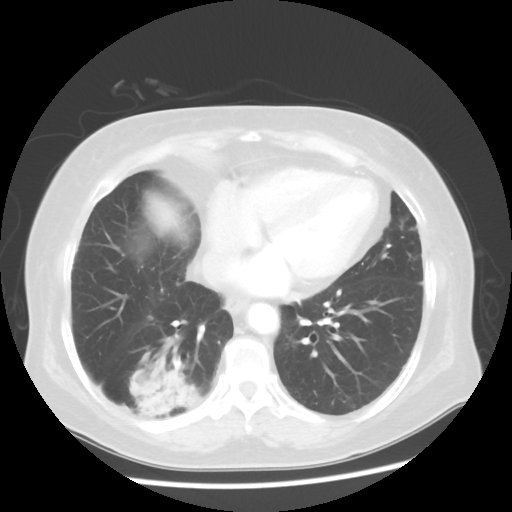
Chest CT, one axial slice. Slice 20 of 56 in the series (ordered by position). Reconstruction kernel STANDARD. 120 kVp. Lung window (W 1500 / L -600 HU). 5 mm slice thickness. 512 × 512 image matrix, field of view 360 × 360 mm. Female patient, age 64 years. From the clinical record (not read from this slice): clinical TNM (as recorded): Tis N0 M0.
Structures marked on this image (rectangle marked by the reading radiologist):
- lung tumour (recorded histology: adenocarcinoma): bounding box [x1, y1, x2, y2] px = [127, 355, 205, 425]